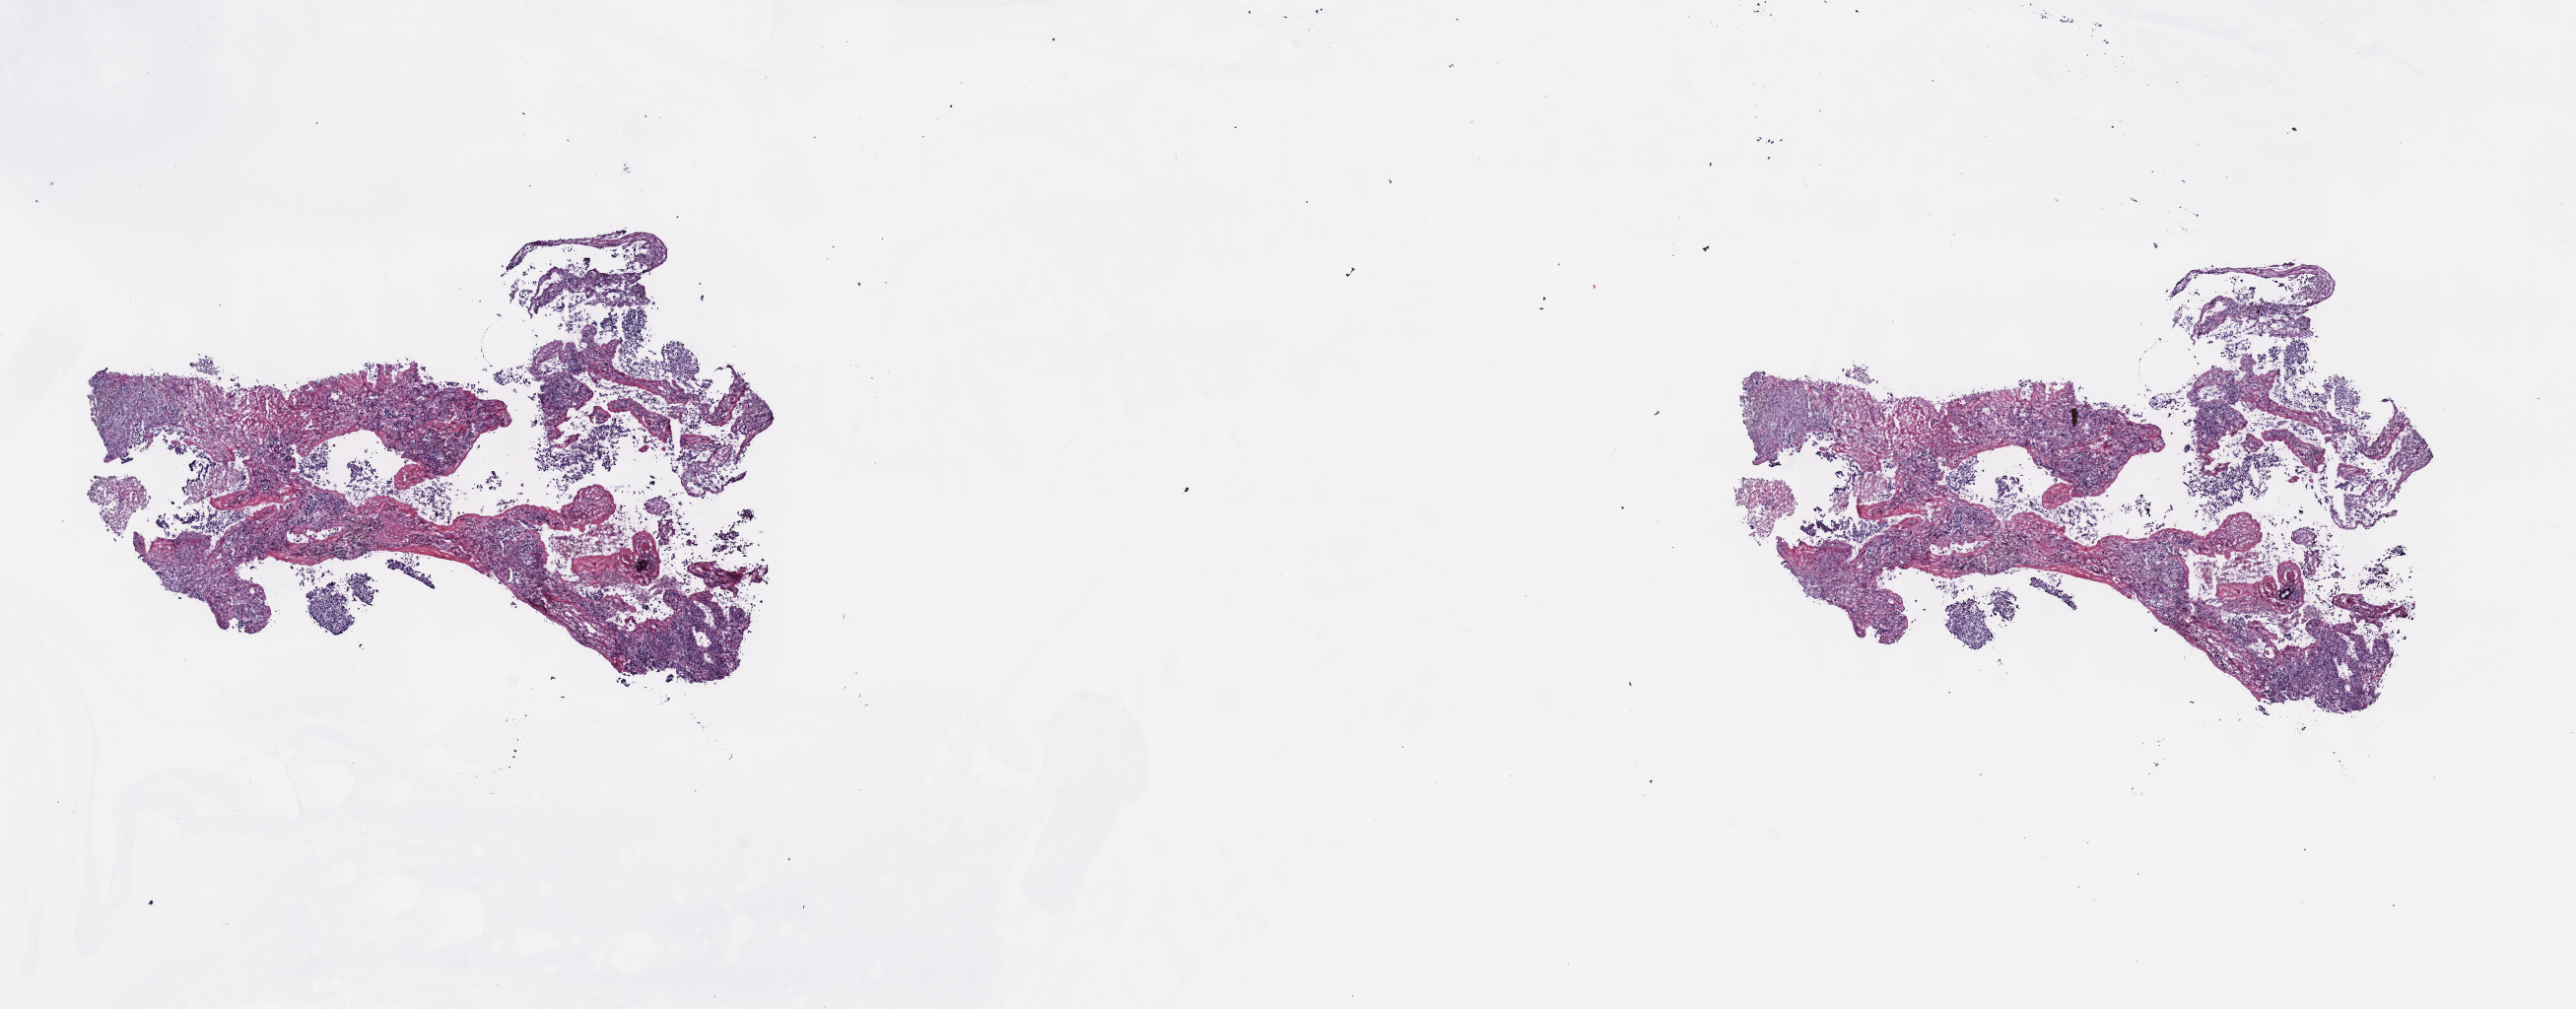
Digitized H&E tissue section (whole slide) — low-resolution overview of the scanned area, about 21.1 x 8.3 mm (acquisition: 40x scan), frozen section from the top of the tissue portion, primary tumour sample from the lung. Female patient; age at initial diagnosis 64 years. Pathologist review of this section (percent, as recorded): tumour cells 70%, tumour nuclei 70%, normal cells 0%, stromal cells 25%, necrosis 5%. Infiltration values recorded for this section: lymphocyte infiltration 40%, monocyte infiltration 20%, neutrophil infiltration 20%.
AJCC pathologic stage: IB (7th edition). Pathologic diagnosis: Adenocarcinoma, NOS (upper lobe, lung). Laterality: left.